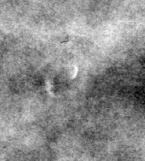
Region of interest cut from a scanned film mammogram (one marked finding), right breast, CC view, BI-RADS breast density category 3 (scale 1–4).
- Calcifications, morphology punctate / pleomorphic, distribution clustered; BI-RADS assessment category 3; pathology (as recorded): malignant.